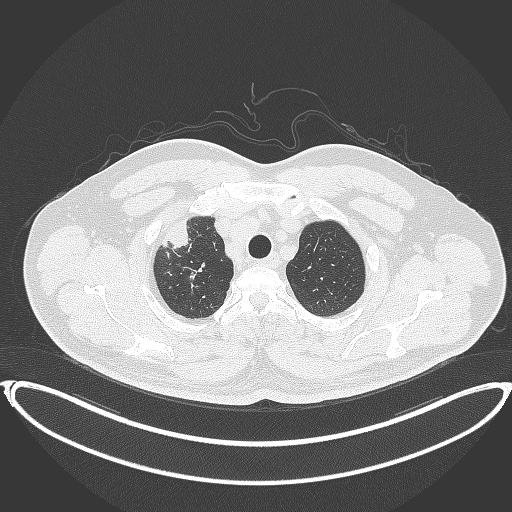
Chest CT, one axial slice; slice 338 of 399 in the series (ordered by position); reconstruction kernel B70f; 120 kVp; lung window (W 1500 / L -600 HU); 512 × 512 image matrix, field of view 445 × 445 mm. Patient: male, 53 years. From the clinical record (not read from this slice): clinical TNM (as recorded): T2a N0 M0.
Outlined on this slice (bounding box drawn by a radiologist):
- lung tumour (recorded histology: adenocarcinoma): bounding box <160,214,193,253> (left, top, right, bottom; pixels)